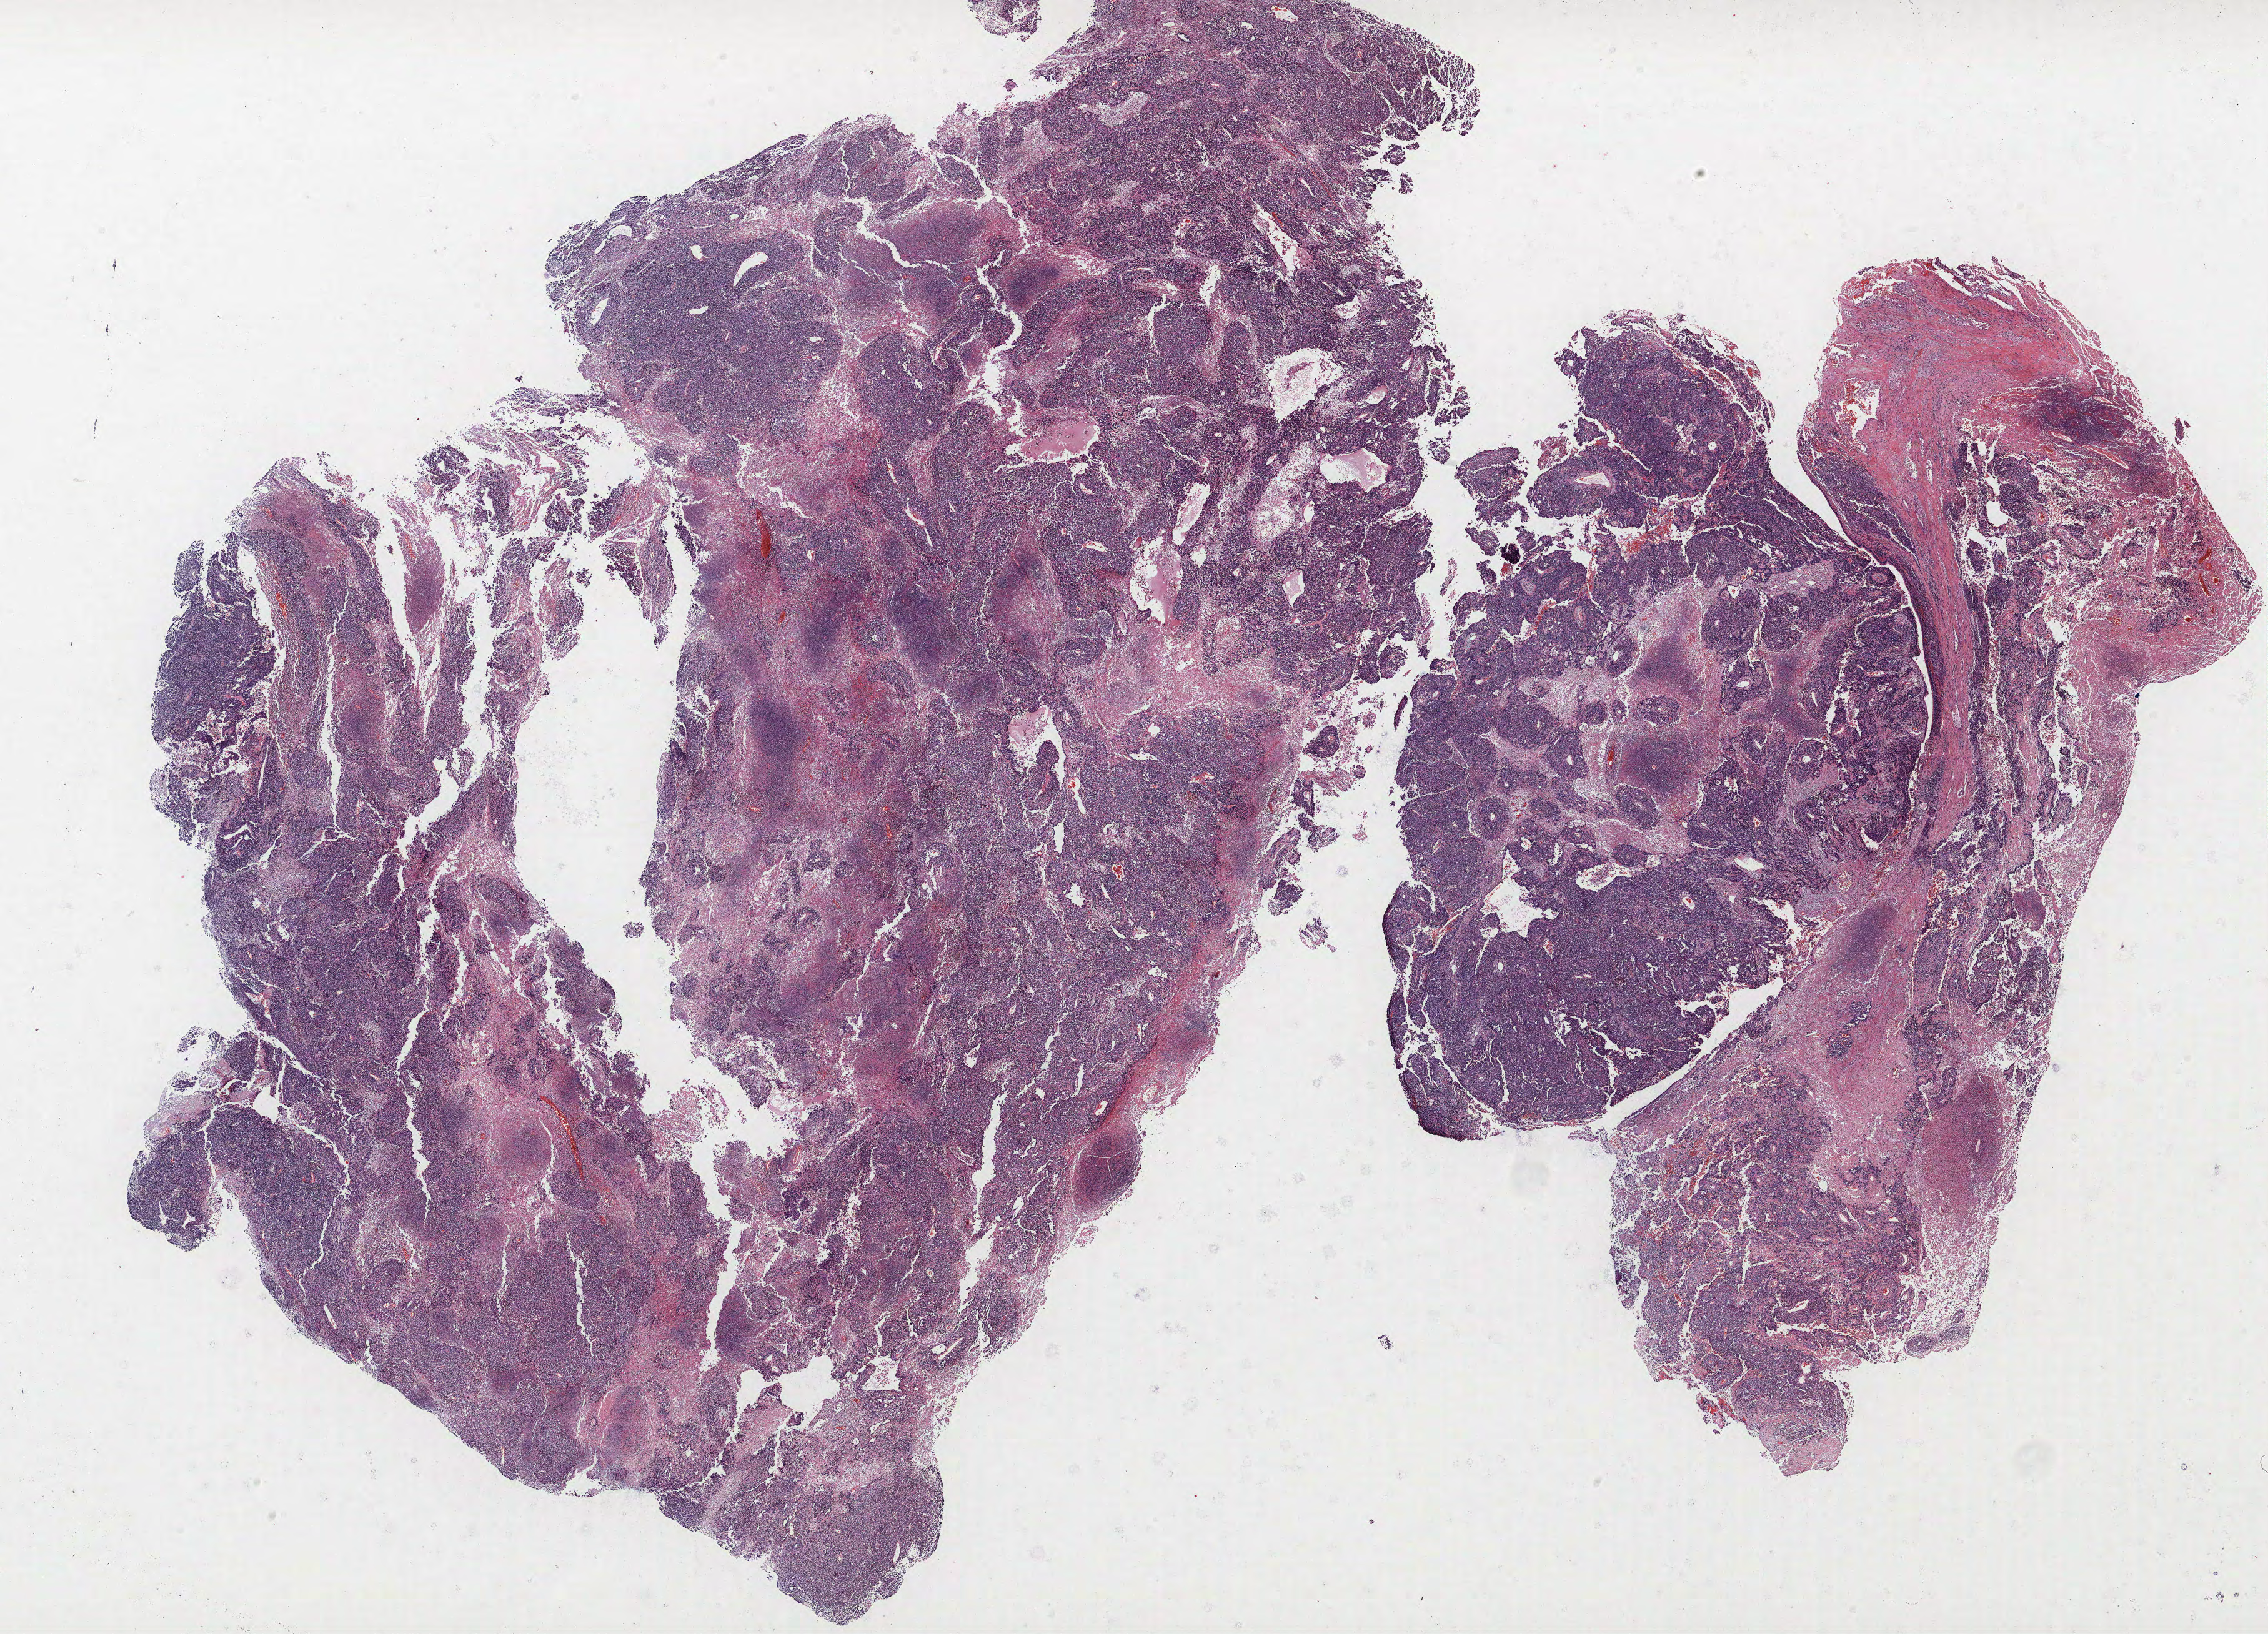
H&E-stained whole-slide image — shown as a low-resolution overview of the whole scanned area (about 29.0 x 20.9 mm, slide scanned at 40x); FFPE section; lung. Male, age 67 at enrolment. Former smoker at enrolment. Grade: poorly differentiated (G3).
* participant's lung-cancer diagnosis: Adenocarcinoma, NOS
* stage (AJCC 6th edition): IB
* tumour size (pathology): 80 mm
* primary tumour location (clinical record): left lower lobe